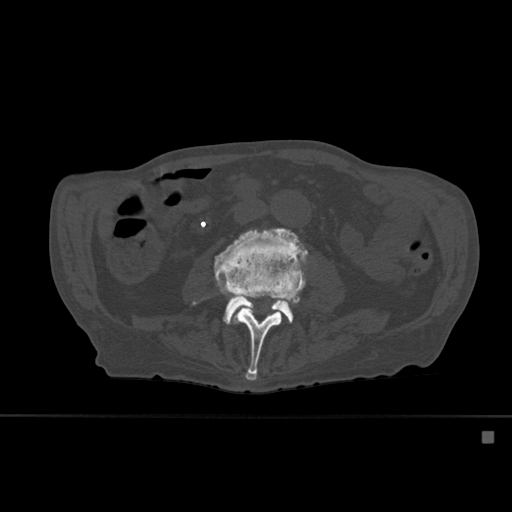
CT including the spine, one axial slice; slice 207 of 527 in the series (ordered by position); bone window (W 1800 / L 400 HU); 512 × 512 image matrix, field of view 373 × 373 mm. Patient: male, 78 years. From the clinical record (not read from this slice): primary cancer: prostate.
Structures marked on this image (semi-automatic segmentation, software-assisted and operator-edited):
- L3 vertebra: bounding box [x1, y1, x2, y2] px = [220, 257, 305, 380]
- L4 vertebra: [193, 227, 308, 324]